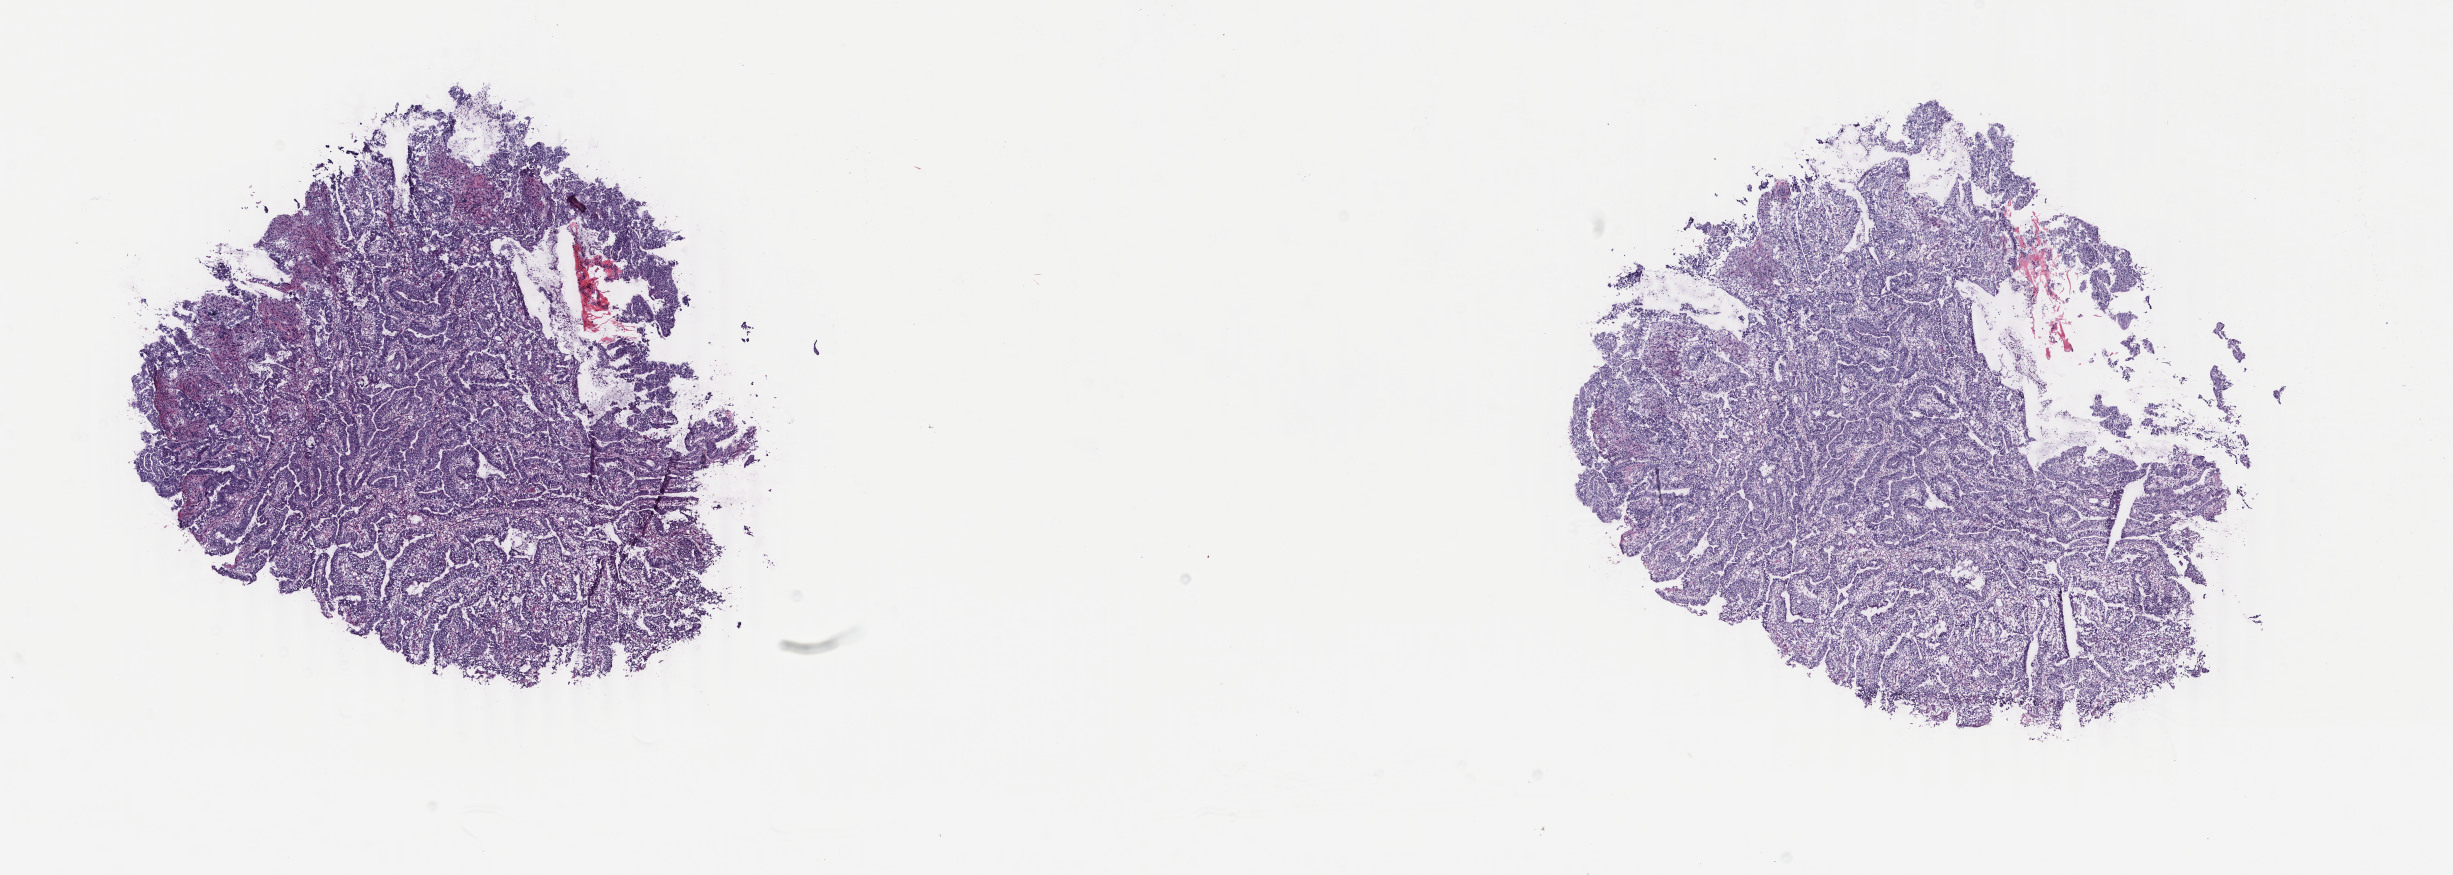
Whole-slide histology image, Hematoxylin and eosin (H&E) stained — low-resolution overview of the scanned area, about 19.5 x 7.0 mm (acquisition: 40x scan), frozen section, rectum, primary tumour sample. Female, age 57 years at initial diagnosis. Composition of this section per pathologist review: tumour cells 85%, tumour nuclei 85%, normal cells 0%, stromal cells 10%, necrosis 5%. Inflammatory infiltration, as recorded: lymphocyte infiltration 2%, monocyte infiltration 0%, neutrophil infiltration 2%.
* diagnosis: Mucinous adenocarcinoma
* AJCC pathologic stage: III (5th edition)
* lymph nodes positive (case pathology): 1 of 12 examined